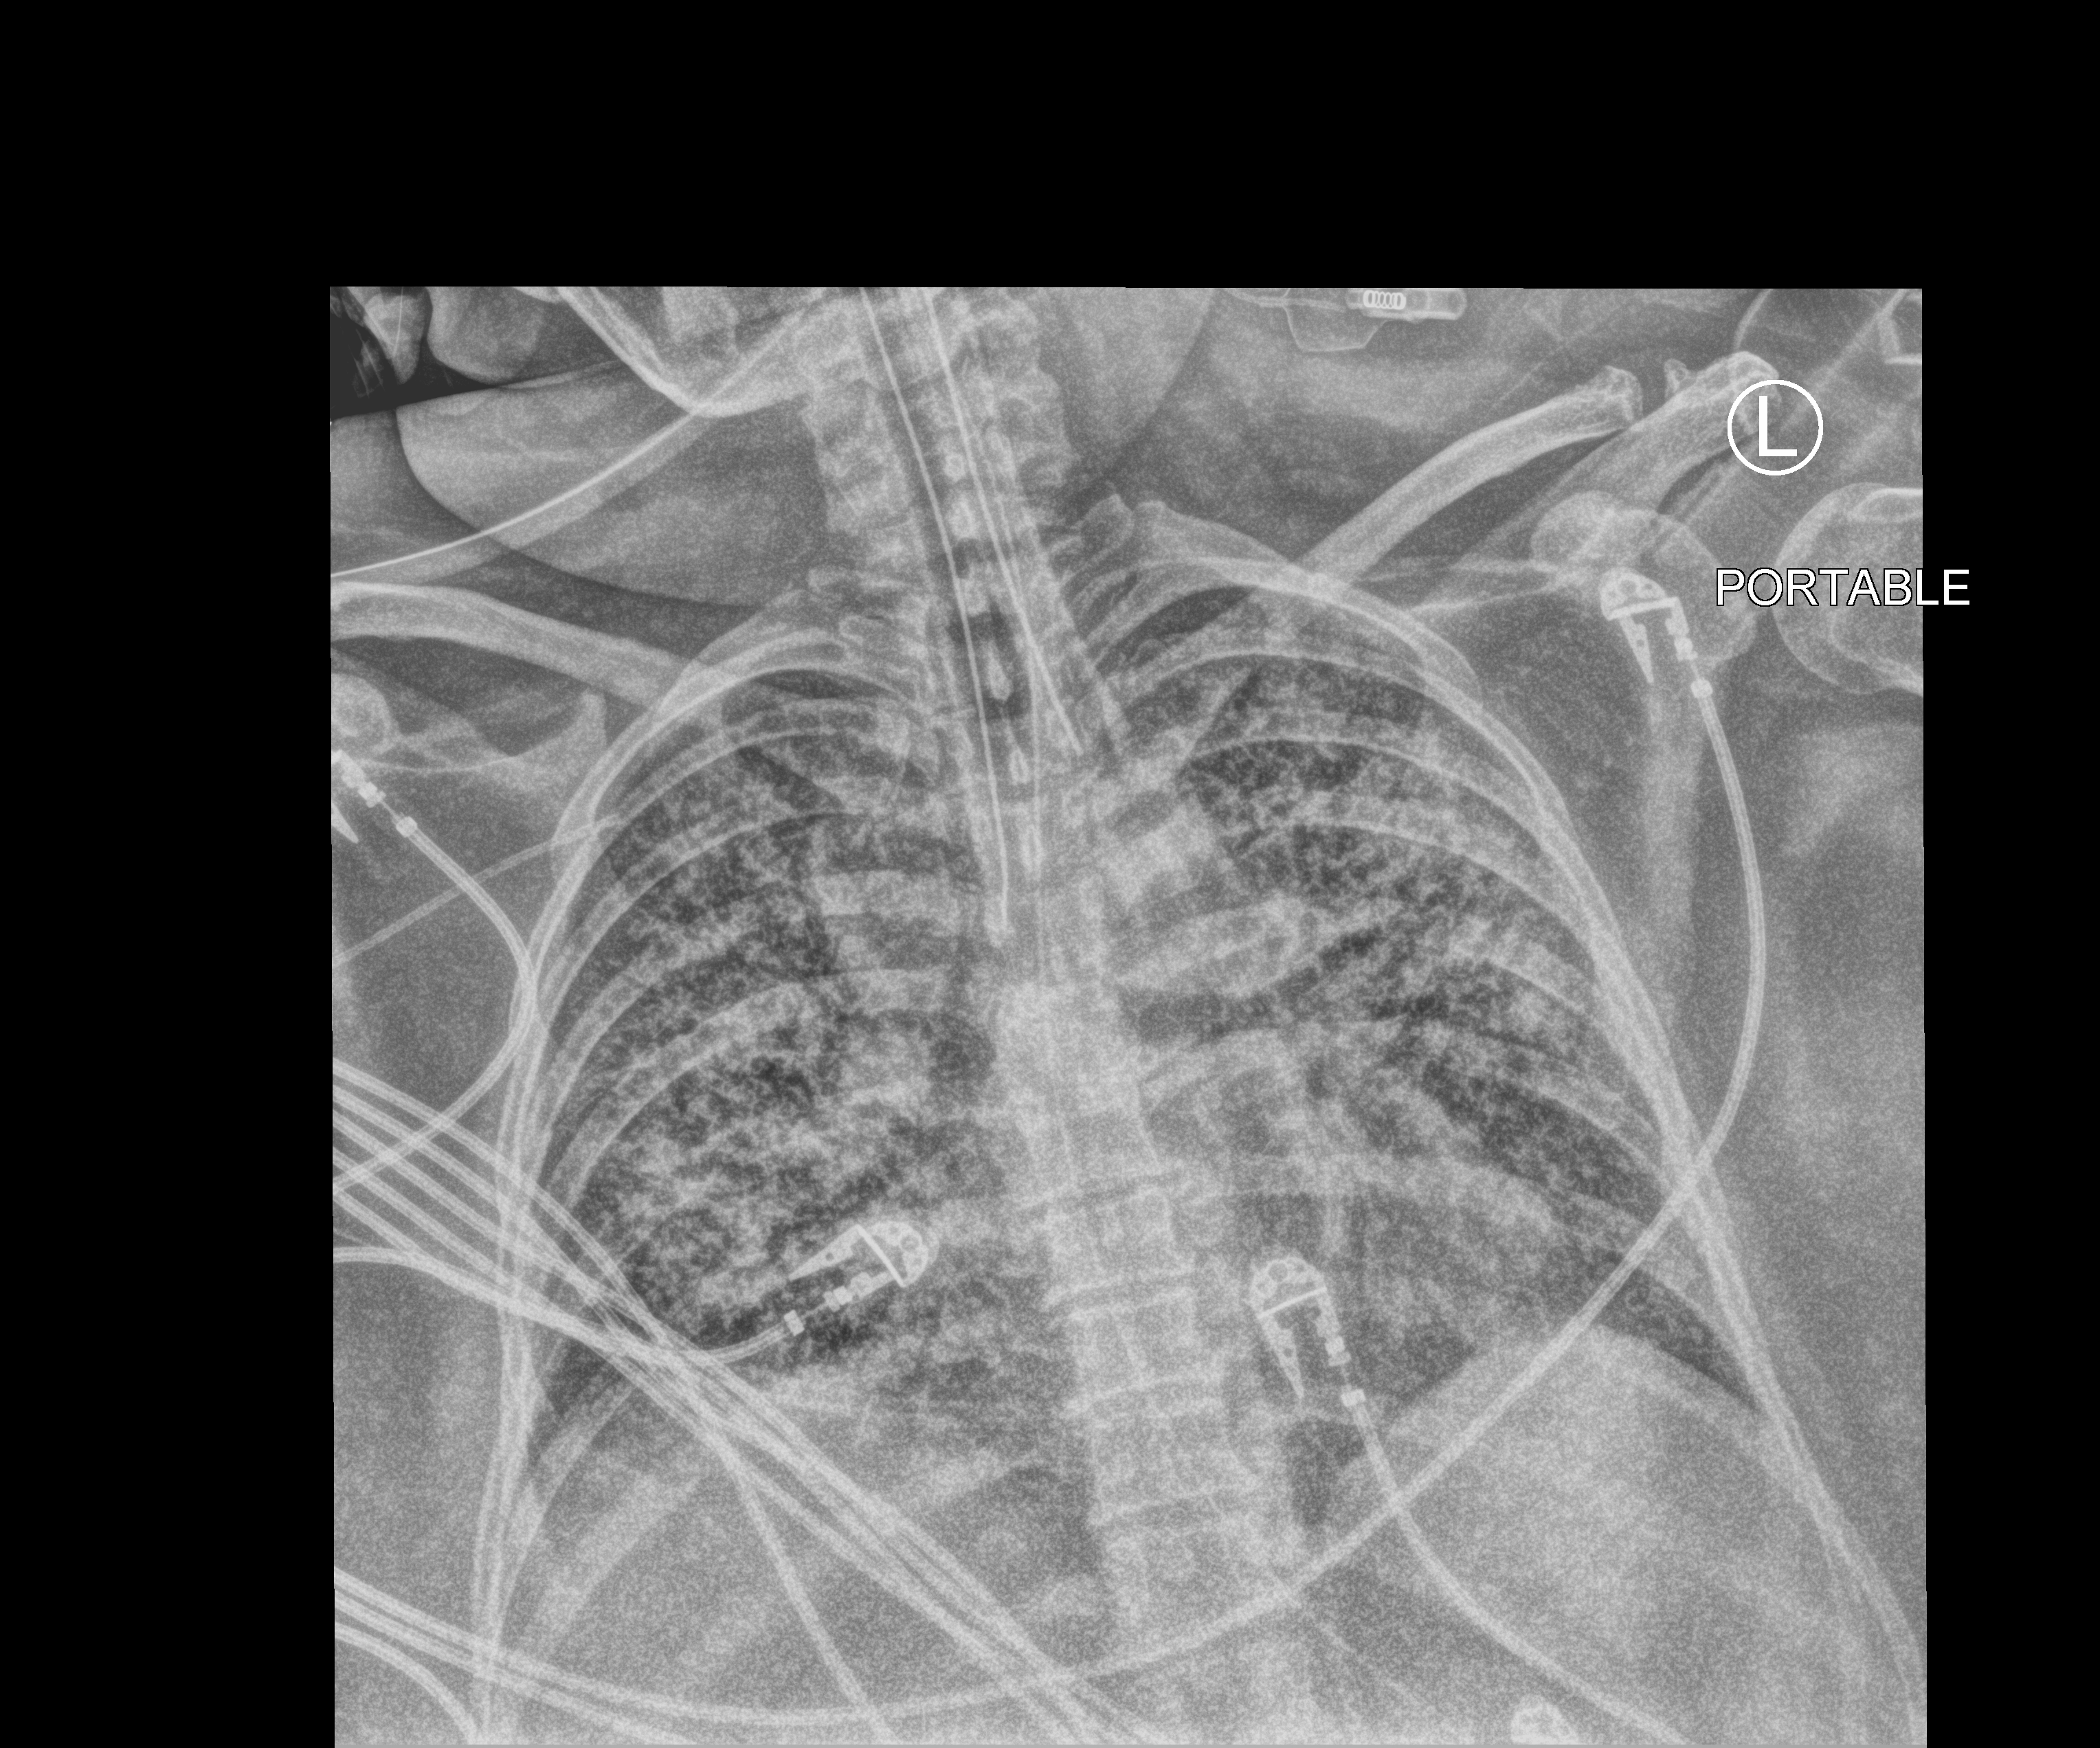
Chest X-ray (portable), anteroposterior (AP) projection. Female patient hospitalised with COVID-19, age 18–59 years.
Hospital-stay facts (about this admission, not read from this image; timing relative to this image not recorded):
- mechanically ventilated during this hospital stay: yes
- COPD (admission record): no